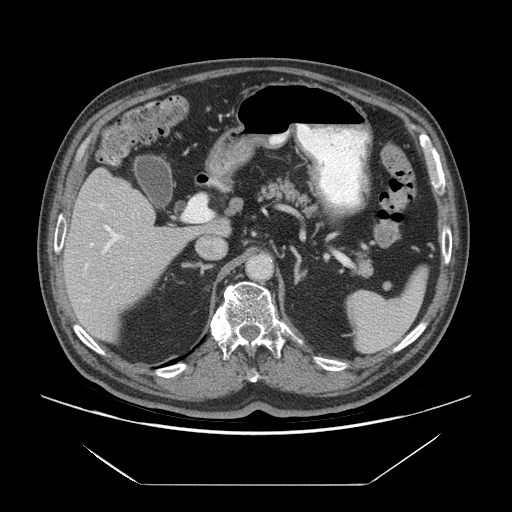
Contrast-enhanced abdominal CT (liver protocol), one axial slice; position 37 of 75 along the scan axis; reconstruction kernel STANDARD; 140 kVp; soft-tissue window (W 400 / L 40 HU); 2.5 mm slice thickness; 512 × 512 image matrix, field of view 420 × 420 mm. From the clinical record (not read from this slice): diagnosis: hepatocellular carcinoma (patient treated with transarterial chemoembolisation; whether this scan precedes or follows treatment is not stated here); TNM stage (as recorded): Stage-I; Child-Pugh class: A; tumour differentiation: well differentiated; tumour nodularity: uninodular.
Annotated regions visible in this slice (semi-automatic segmentation, software-assisted and operator-edited):
- liver parenchyma outside the tumour (the mass and vessels are separate outlines, so this box may not span the whole liver): bounding box (x1, y1, x2, y2) in pixels: (62, 168, 195, 342)
- liver vessels: (83, 203, 124, 302)